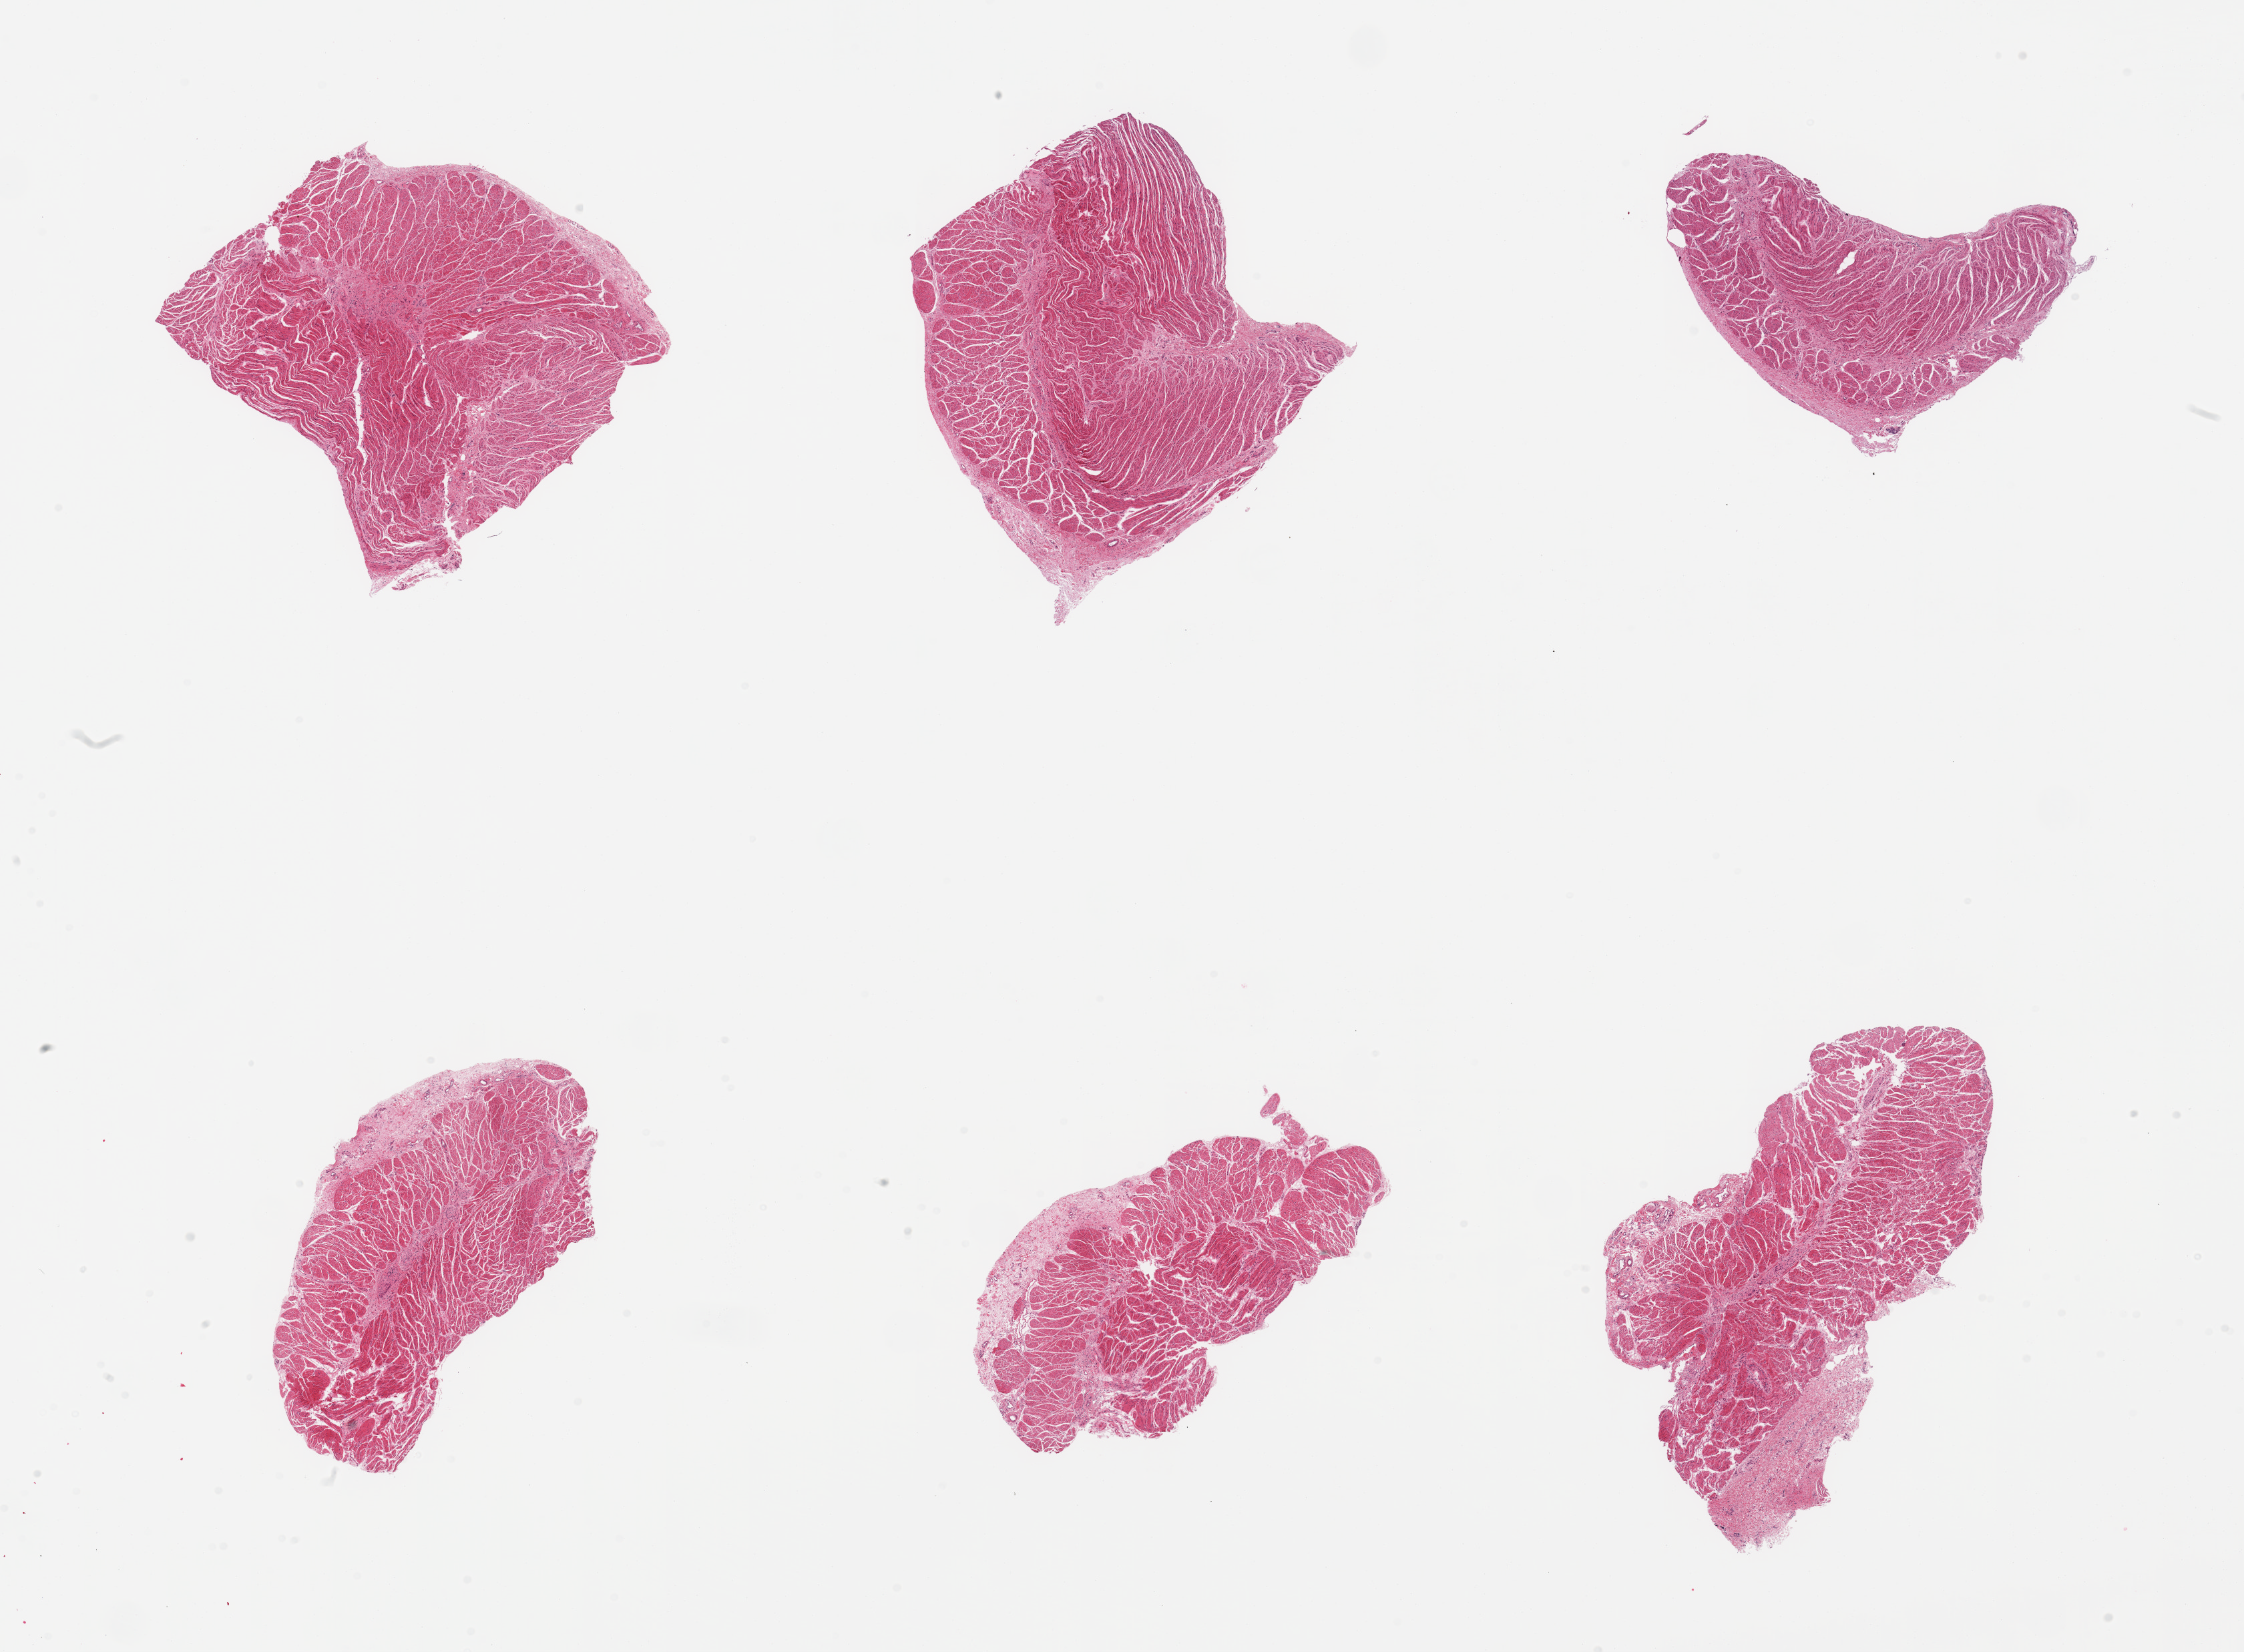
Whole-slide image, hematoxylin and eosin (H&E) stain, shown as a low-resolution overview of the whole scanned area (about 26.6 x 19.6 mm). PAXgene-fixed paraffin-embedded (PFPE) section. Section of gastroesophageal junction (target tissue). Donor tissue sample. Donor sex: female.
Reviewer comment on this tissue sample: 6 pieces; up to 10% fibrous content.